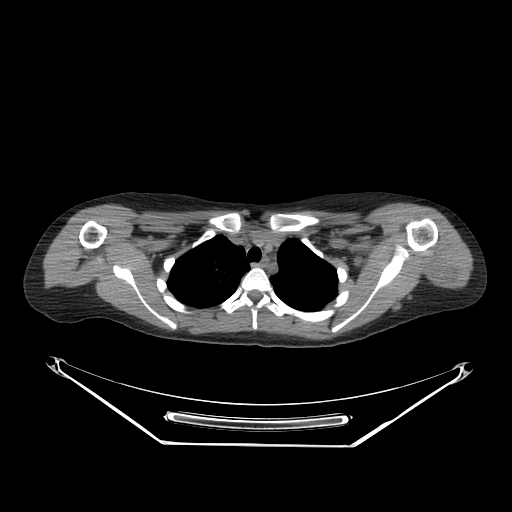
CT of an extremity soft-tissue mass (from a PET/CT study), one axial slice; position 209 of 267 along the scan axis; reconstruction kernel SOFT; 140 kVp; soft-tissue window (W 400 / L 40 HU); 3.75 mm slice thickness; 512 × 512 image matrix, field of view 500 × 500 mm. Female patient. Case-level facts recorded for this patient, not image findings: histological type: malignant fibrous histiocytoma; grade: low; site of the primary tumour: left arm.
Outlined on this slice (expert contour drawn on MRI and transferred to this co-registered scan by the dataset authors):
- gross tumour volume (mass): box from (x=423, y=253) to (x=458, y=284) px